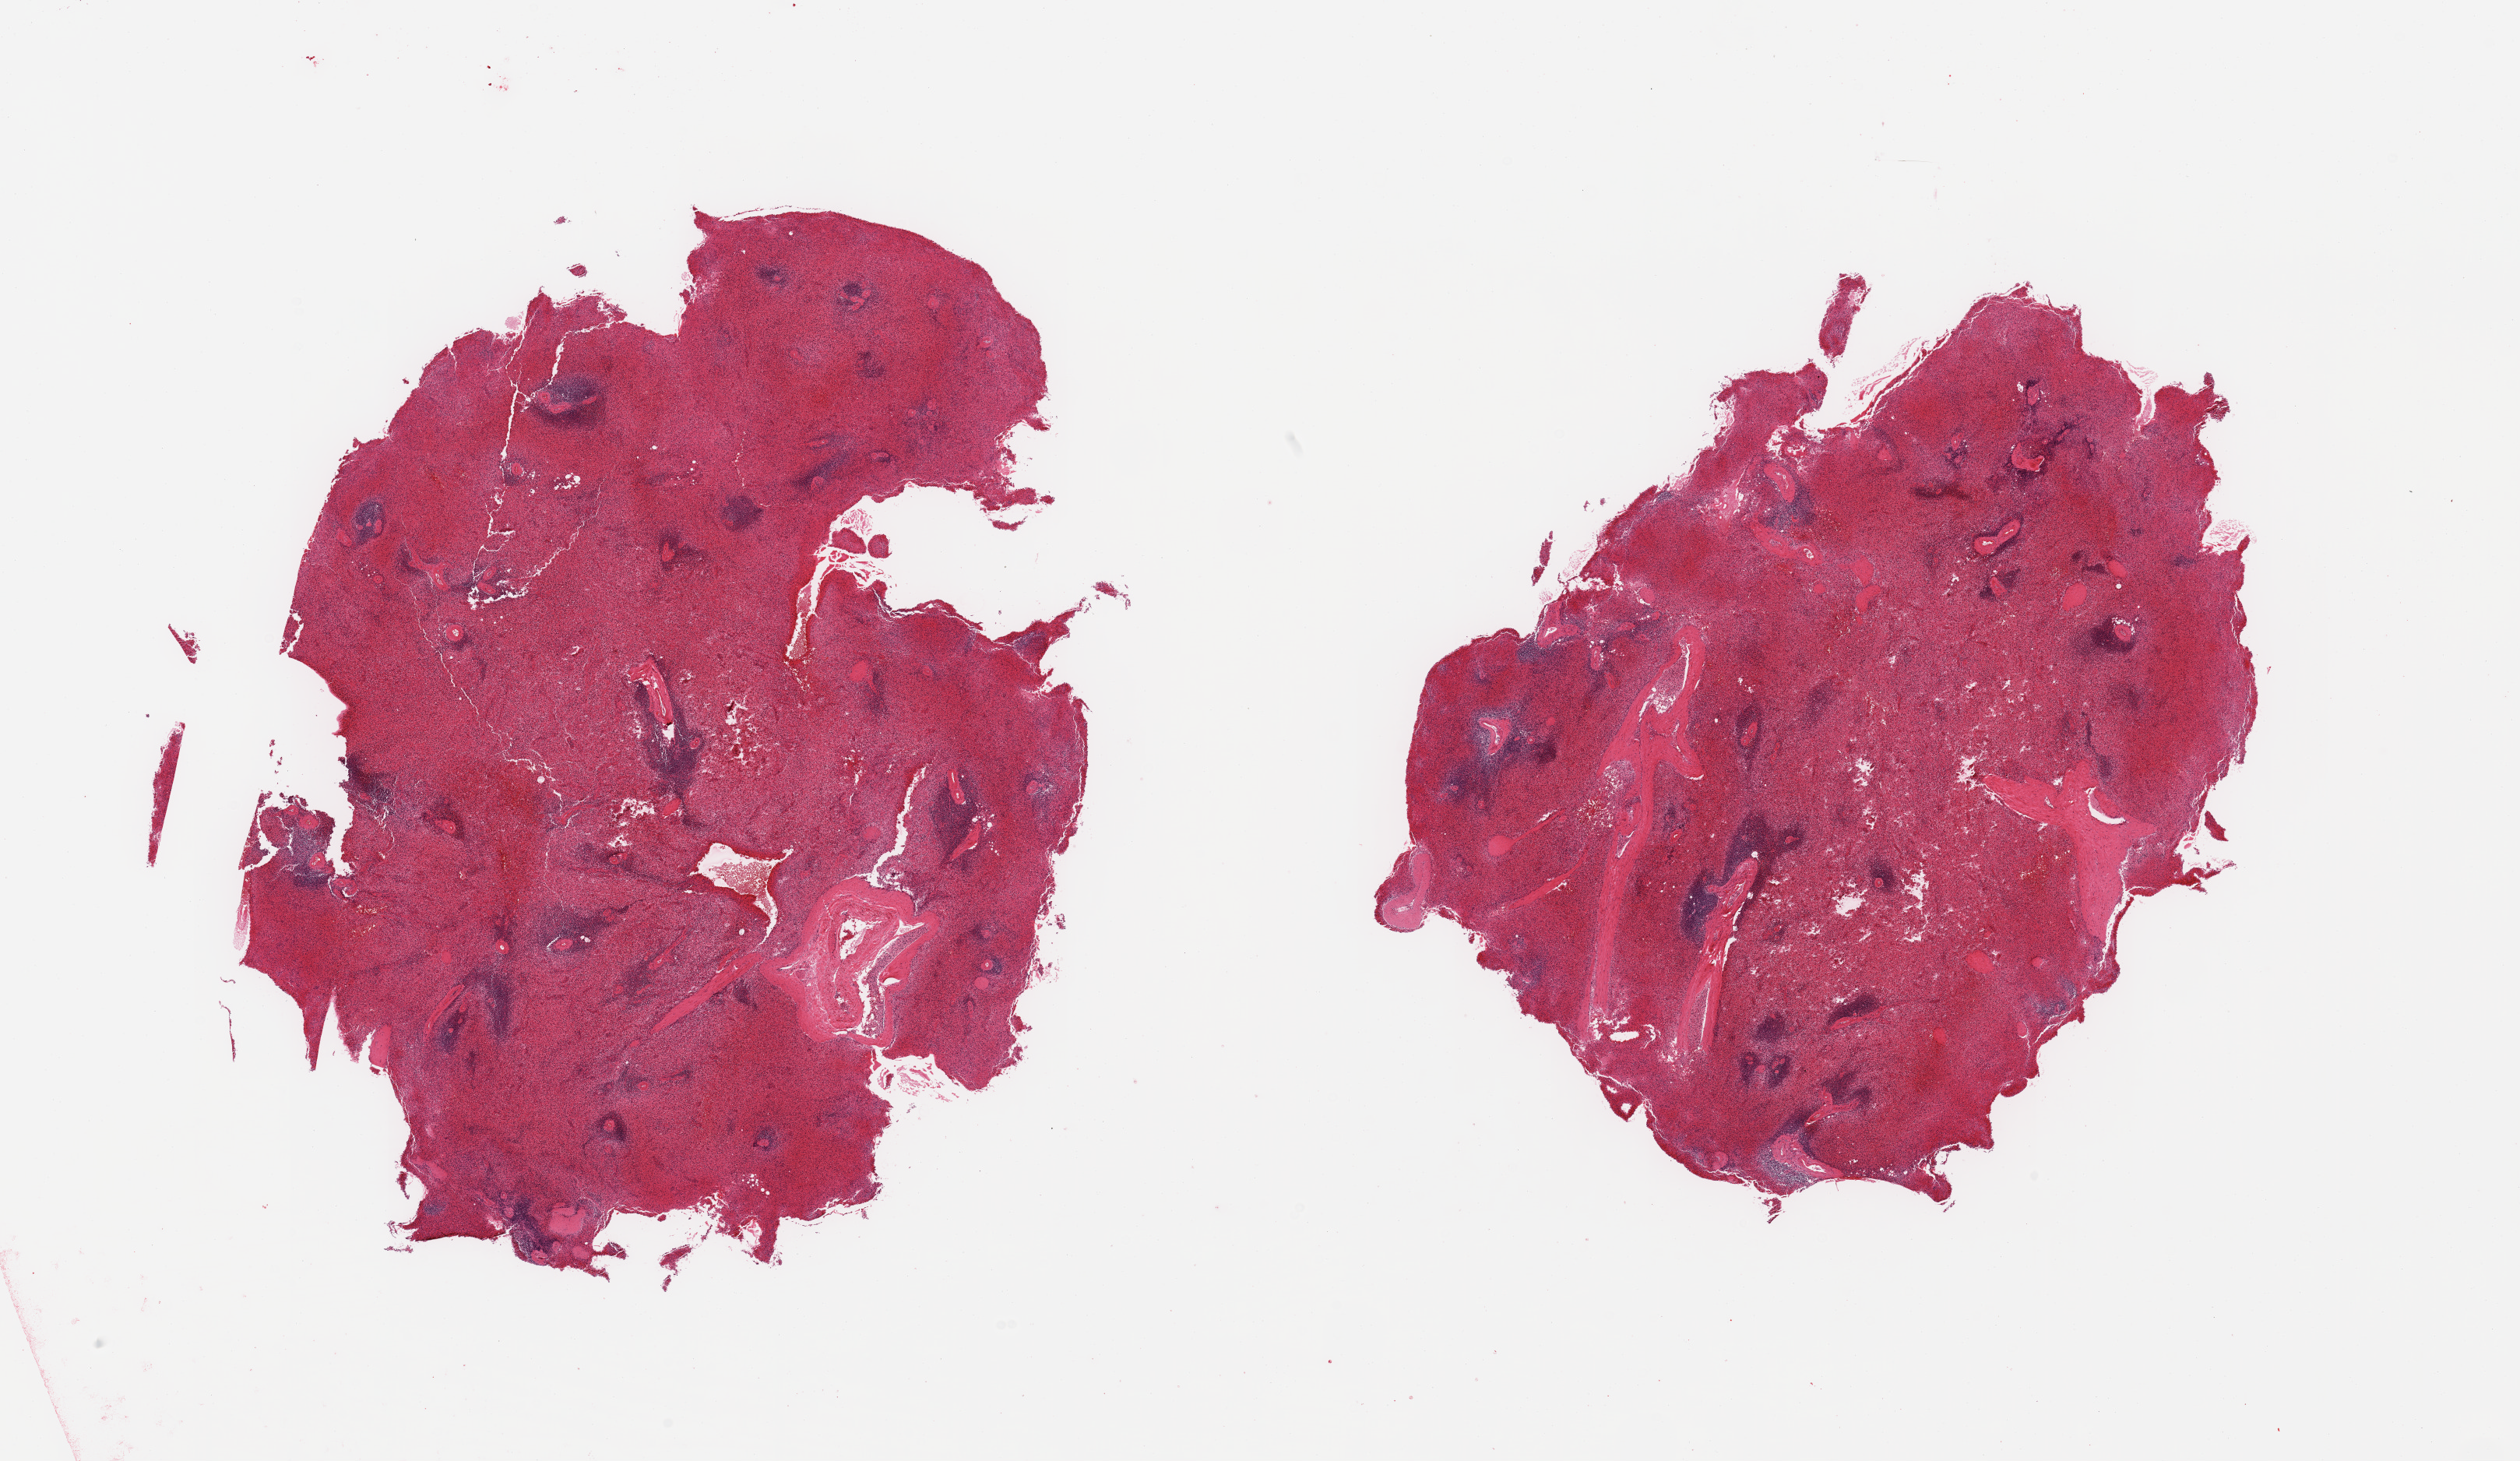
Whole-slide image, H&E stain, brightfield, whole scanned area (about 25.6 x 14.8 mm) shown as a low-resolution overview. PAXgene-fixed paraffin-embedded (PFPE) section. Sampled site (target tissue): spleen. Donor tissue sample. Donor sex: male.
• review note (as recorded): 2 pieces; congested